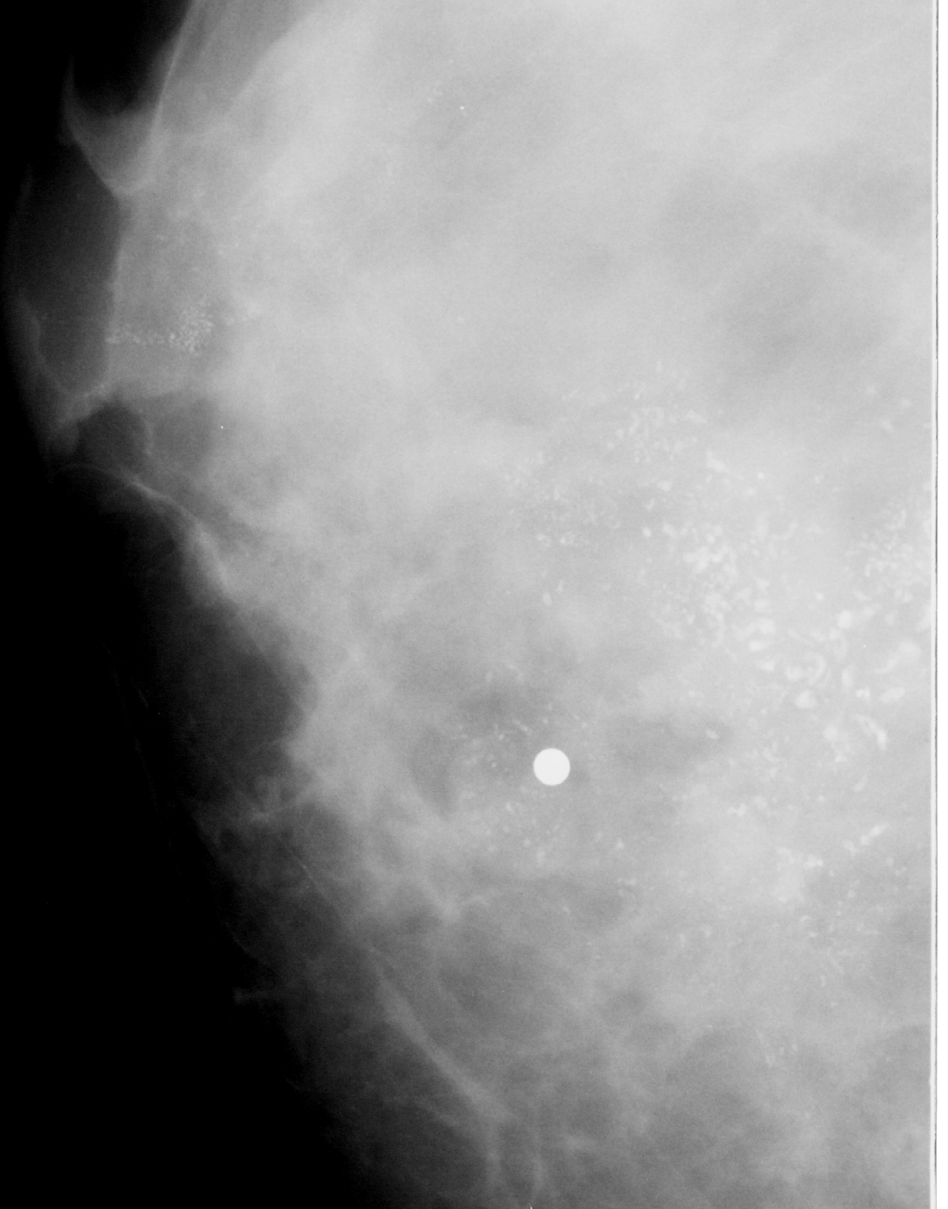
Crop from a digitized film mammogram around one marked abnormality; right breast; CC view.
Marked abnormality: calcifications, morphology pleomorphic, distribution regional; BI-RADS assessment category 5; pathology result (as recorded, not read from the image): malignant.